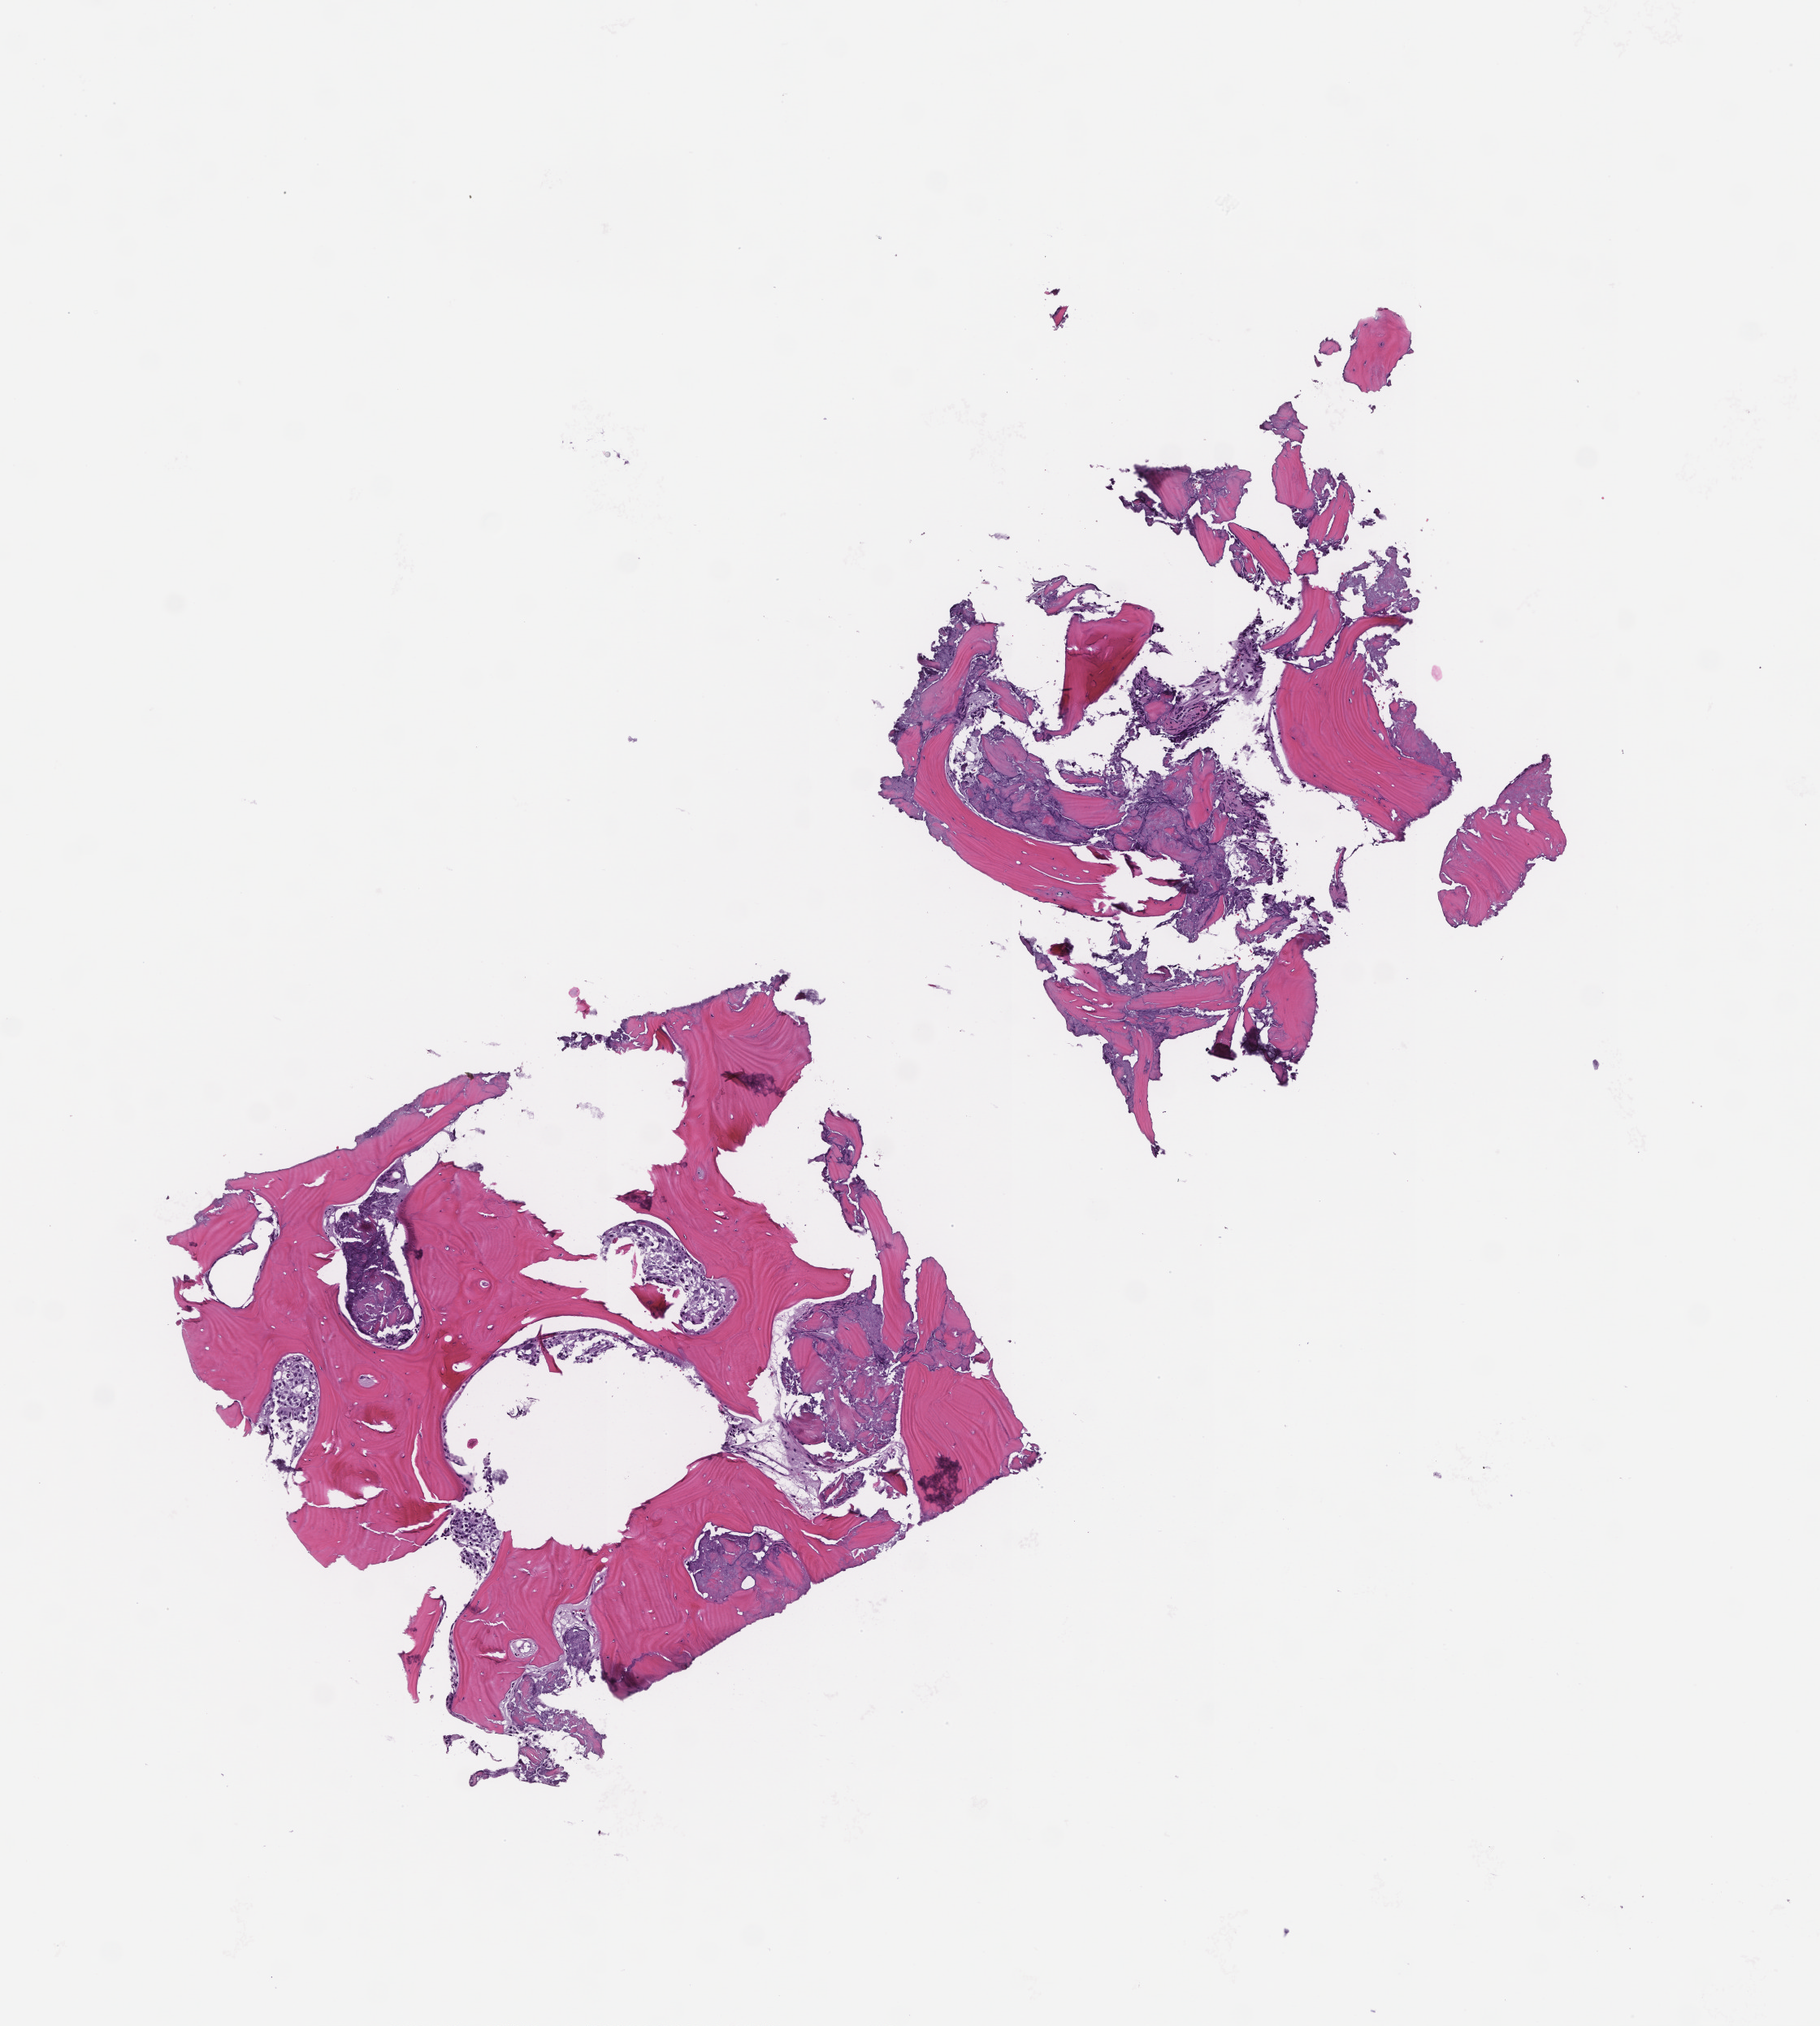
Whole-slide image, hematoxylin and eosin (H&E) stain — low-resolution overview of the scanned area, about 4.5 x 5.0 mm, FFPE section, collected at disease progression. Patient: male.
This section: metastatic tumor tissue. Patient diagnosis (primary): Prostate Carcinoma.